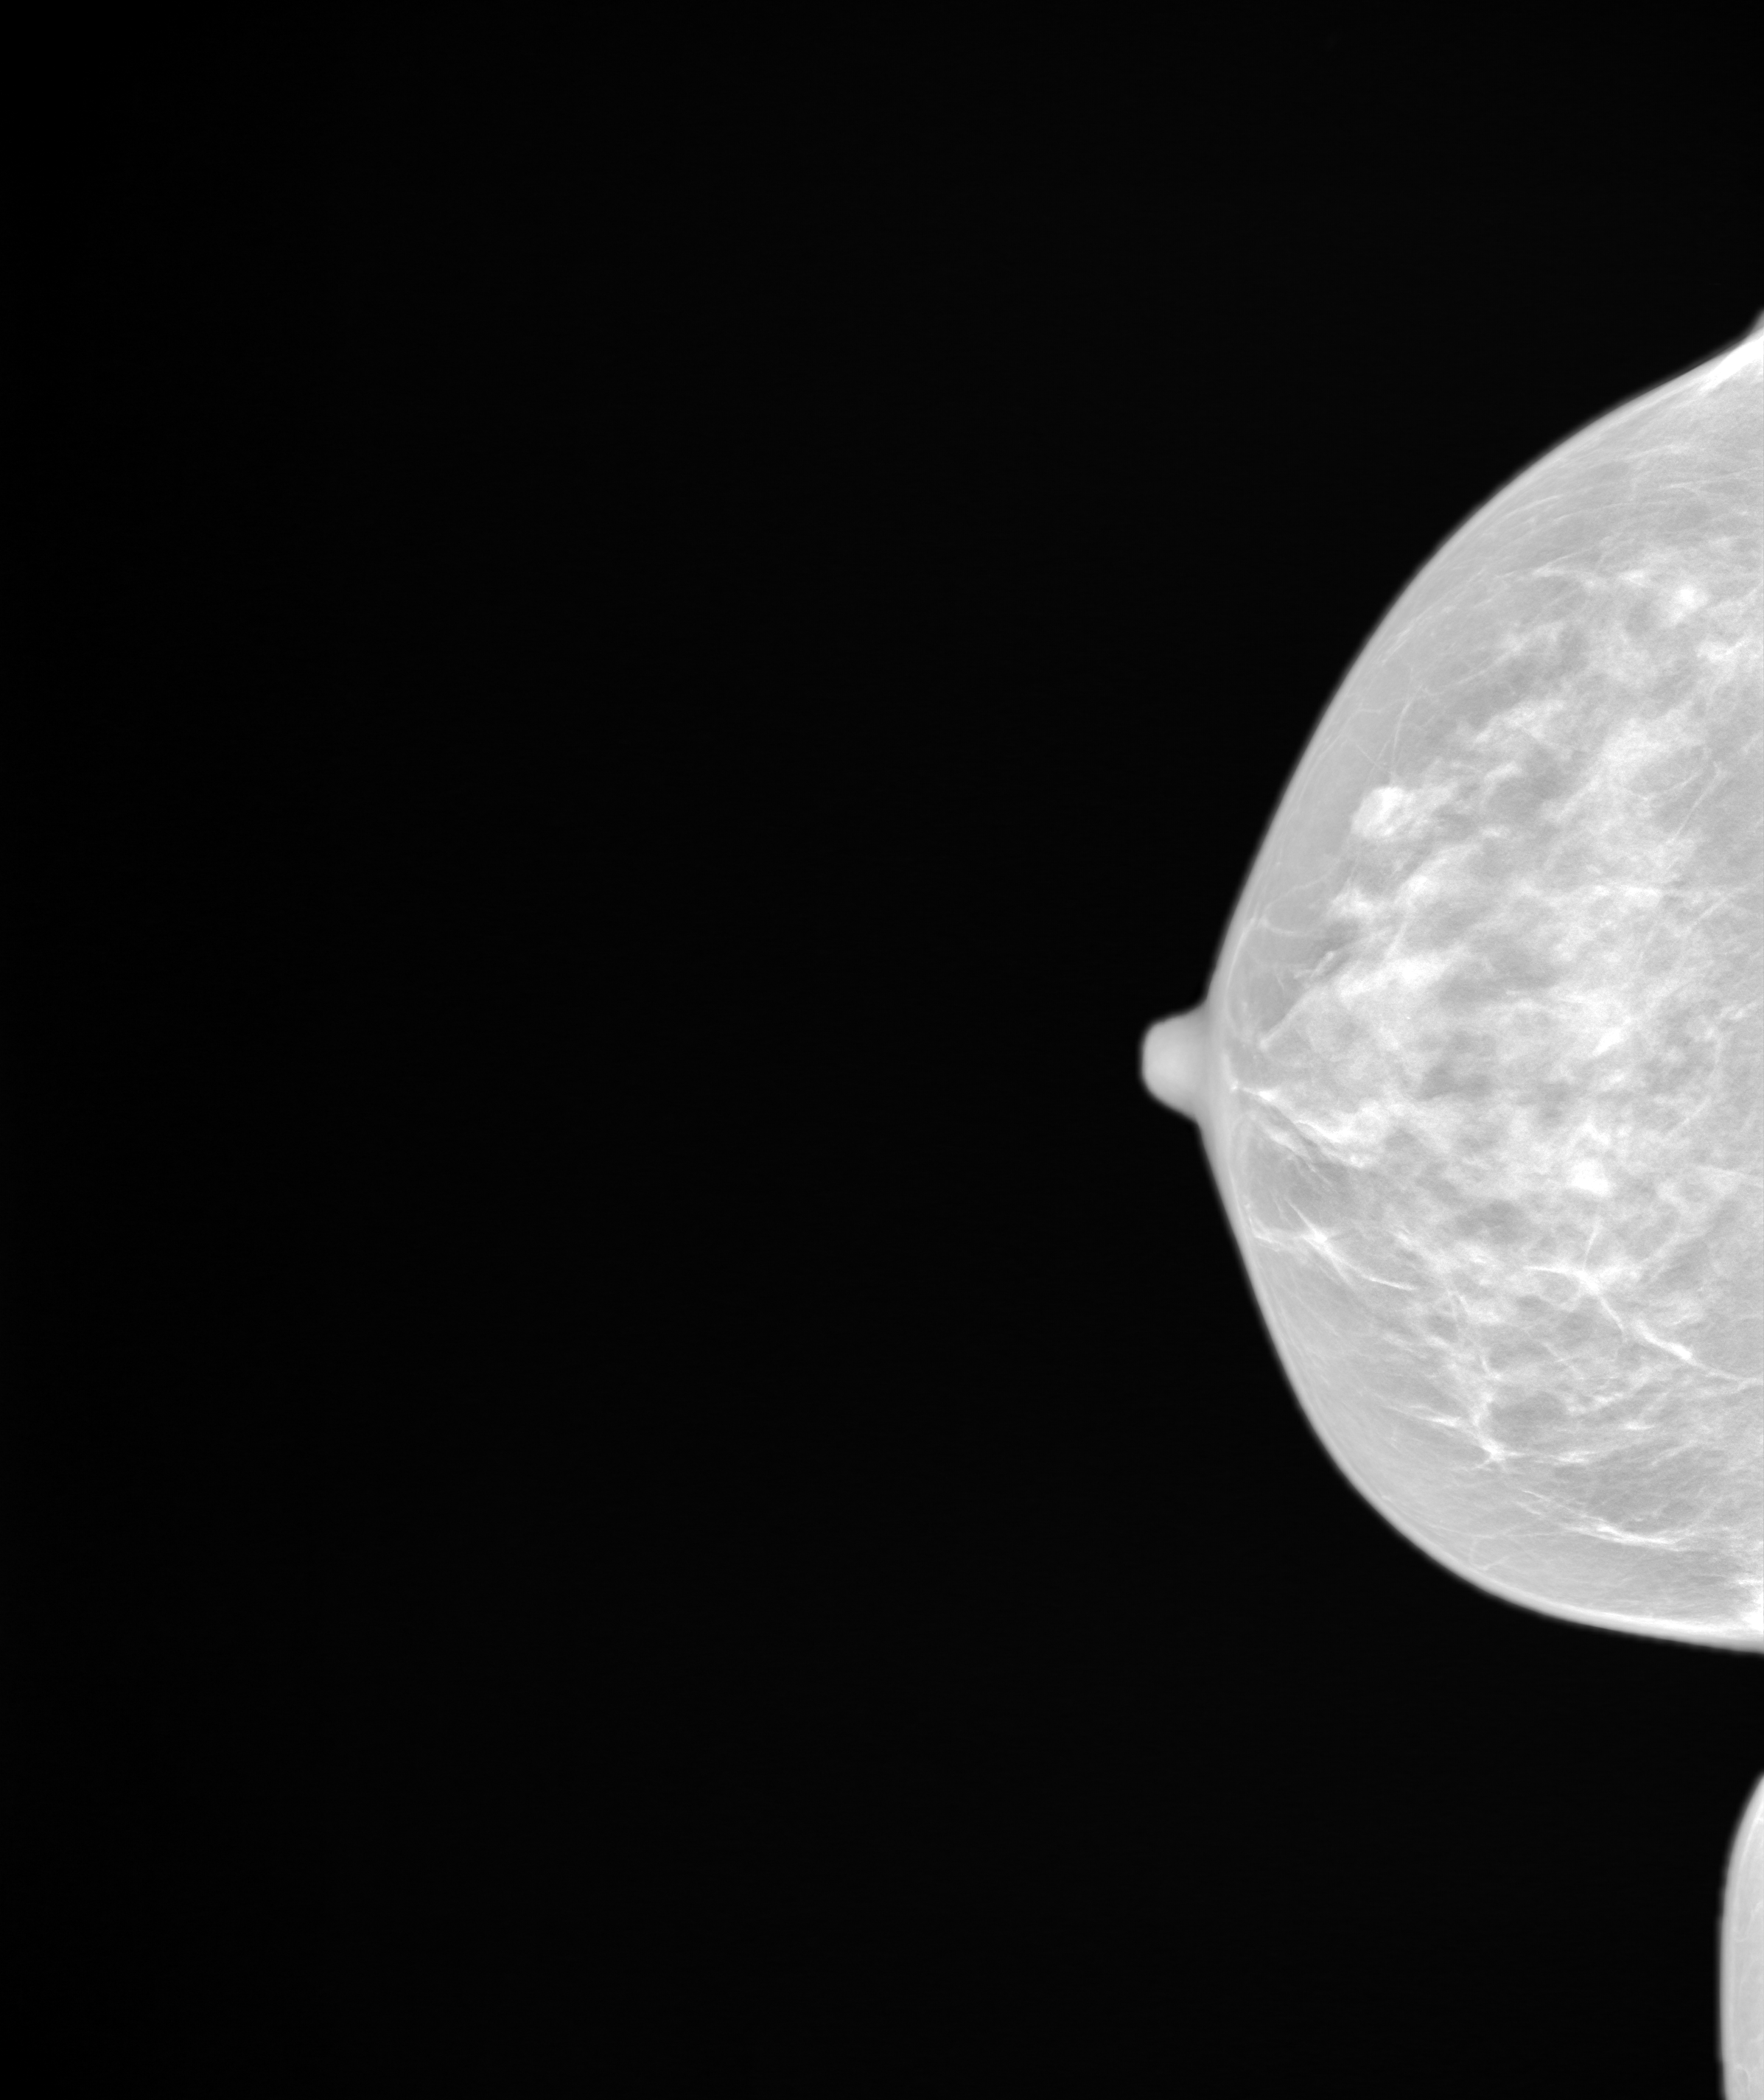
Screening examination; system: SenoIris_1SP2(440). Patient aged 59 years (female).
Image type: synthesized 2-D view from tomosynthesis. Breast: right. Projection: cranio-caudal projection.